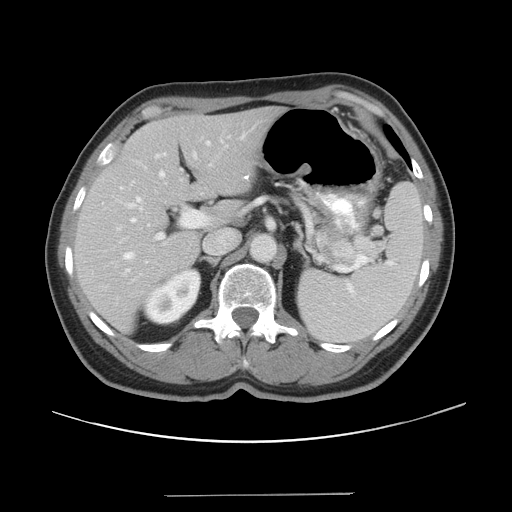
Contrast-enhanced abdominal CT, one axial slice. Position 25 of 43 along the scan axis. Intravenous contrast given. Soft-tissue window (W 400 / L 40 HU). 5 mm slice thickness. 512 × 512 image matrix, field of view 409 × 409 mm. Male patient, age 65 years. From the clinical record (not read from this slice): diagnosis: colorectal cancer liver metastases, imaged before liver resection; multiple liver metastases: no; largest metastasis: 3.8 cm; chemotherapy before resection: yes.
Outlined on this slice (expert manual segmentation):
- hepatic veins: bounding box [x1, y1, x2, y2] px = [117, 159, 167, 272]
- liver: [75, 108, 277, 330]
- planned liver remnant (the part of the liver to remain after resection): [75, 109, 276, 330]
- portal vein (with intrahepatic branches): [117, 135, 231, 247]